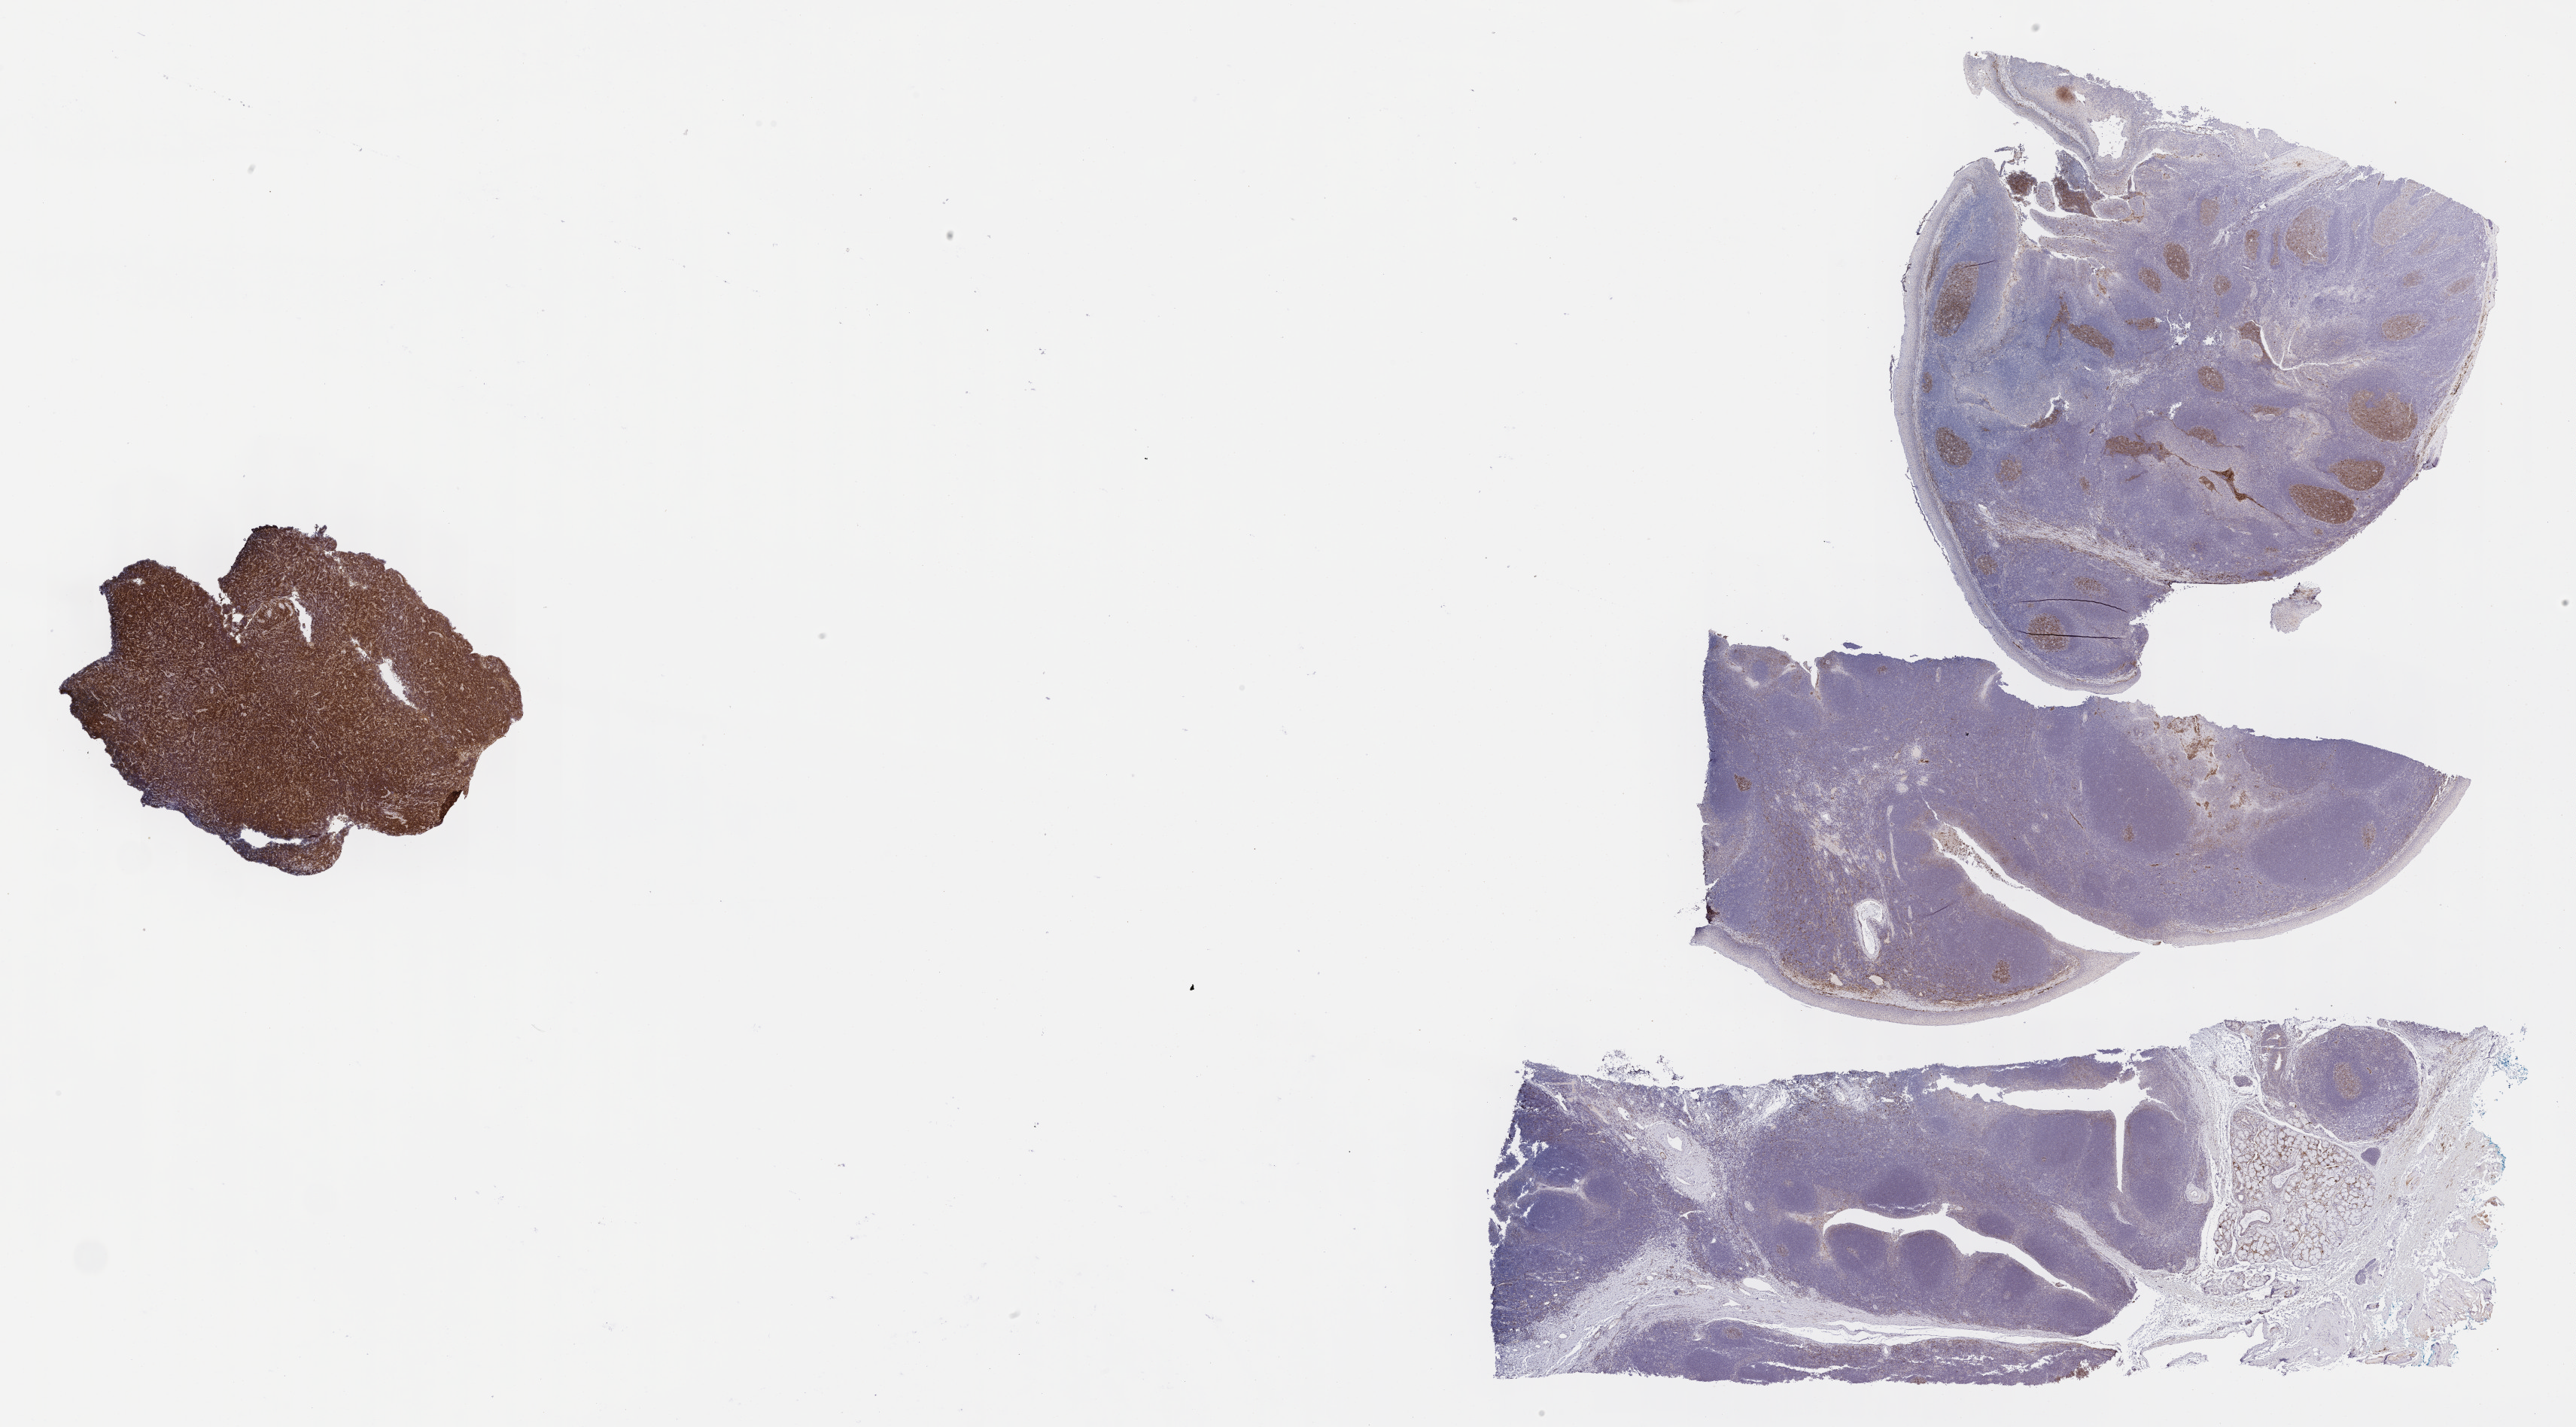
IHC for CD10, whole-slide image — low-resolution overview of the scanned area, about 27.7 x 15.3 mm. Specimen: tumor tissue. Site: mandible. Male patient; age at initial diagnosis 8 years.
Diagnosis: Burkitt lymphoma, NOS.